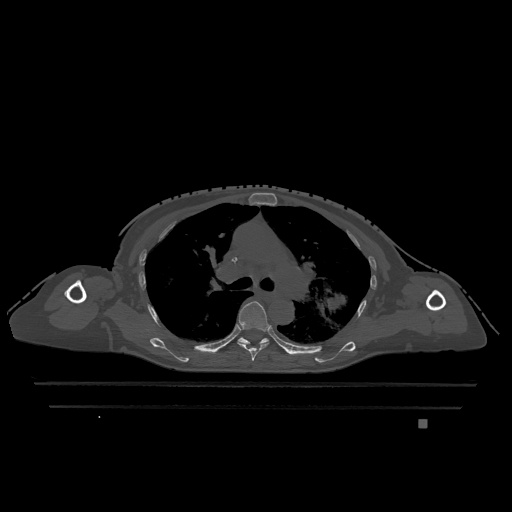
CT including the spine, one axial slice; position 819 of 1317 along the scan axis; bone window (W 1800 / L 400 HU); 512 × 512 image matrix. Female patient, age 74 years. From the clinical record (not read from this slice): primary cancer: lung; vertebrae with lytic lesions (as recorded): T1, T4, T5, T6, L4, L5.
Annotated regions visible in this slice (semi-automatically segmented with operator editing):
- T5 vertebra: bounding box <238,301,269,361> (left, top, right, bottom; pixels)
- T6 vertebra: <238,337,269,344>